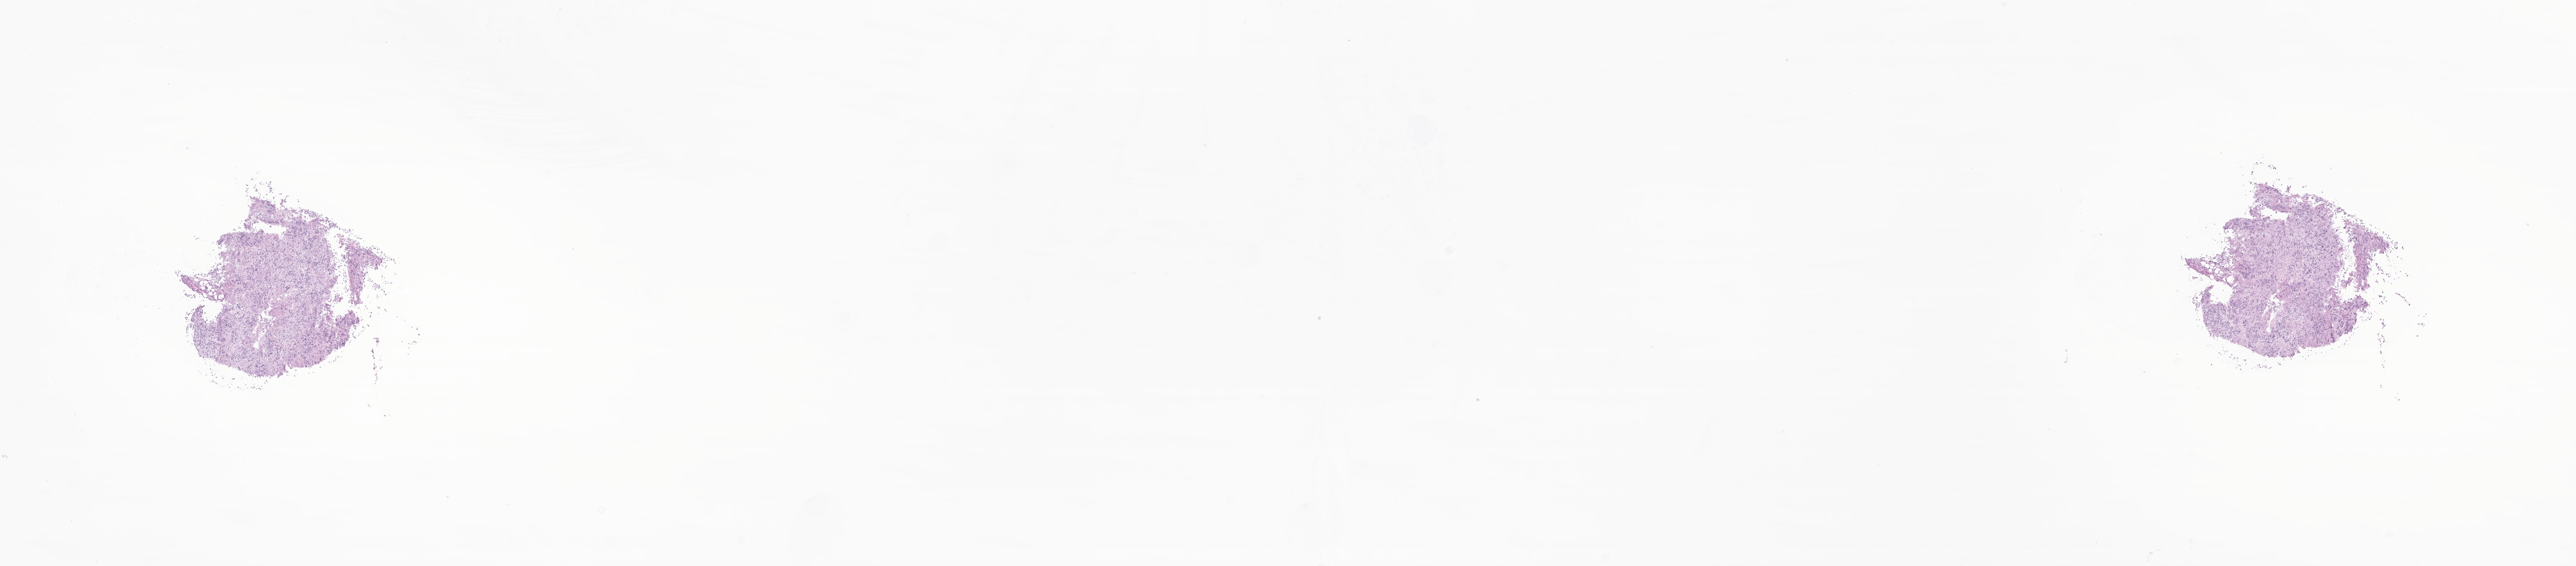
Digitized haematoxylin and eosin-stained section of tumor tissue from the adrenal gland, shown as a low-resolution overview of the whole scanned area (about 27.3 x 6.0 mm); cryosection (OCT / tissue freezing medium). Patient female; age 108 months.
- diagnosis: Neuroblastoma, NOS